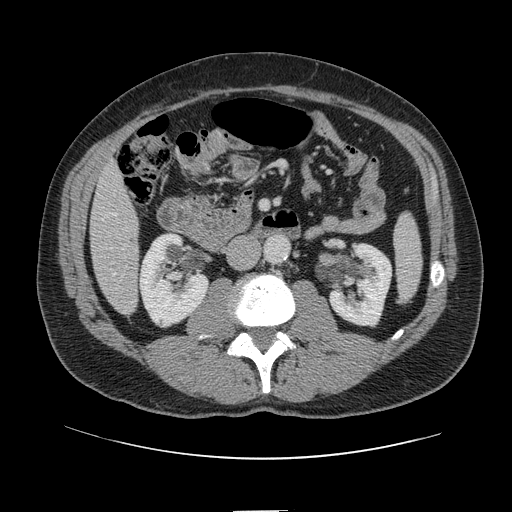
Contrast-enhanced abdominal CT, one axial slice. Position 28 of 161 along the scan axis. 120 kVp. Intravenous contrast given. Soft-tissue window (W 400 / L 40 HU). 2.5 mm slice thickness. 512 × 512 image matrix. Male patient, age 66 years. Case-level facts recorded for this patient, not image findings: diagnosis: colorectal cancer liver metastases, imaged before liver resection; multiple liver metastases: no; largest metastasis: 3.5 cm; disease in both lobes: no.
Structures marked on this image (manually delineated by an expert):
- hepatic veins: box from (x=114, y=213) to (x=117, y=275) px
- liver: (x=92, y=166)–(x=140, y=314)
- planned liver remnant (the part of the liver to remain after resection): (x=92, y=166)–(x=138, y=258)